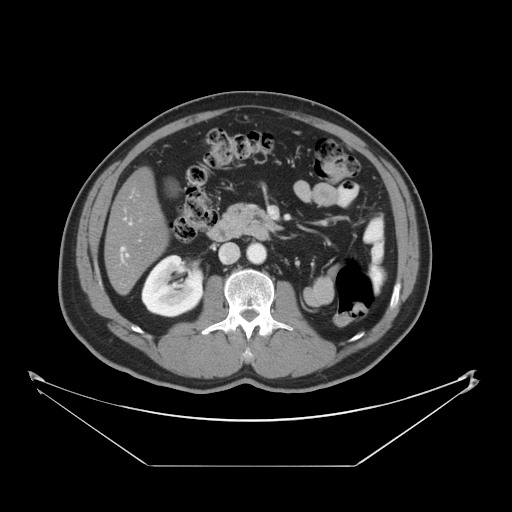
Contrast-enhanced abdominal CT, one axial slice; slice 16 of 46 in the series (ordered by position); reconstruction kernel STANDARD; 120 kVp; intravenous contrast given; soft-tissue window (W 400 / L 40 HU); 5 mm slice thickness; 512 × 512 image matrix, field of view 465 × 465 mm. Male patient, age 57 years. Case-level facts recorded for this patient, not image findings: diagnosis: colorectal cancer liver metastases, imaged before liver resection; multiple liver metastases: no; largest metastasis: 3.3 cm.
Annotated regions visible in this slice (manually delineated by an expert):
- hepatic veins: box from (x=121, y=247) to (x=124, y=250) px
- liver: (x=105, y=170)–(x=168, y=293)
- planned liver remnant (the part of the liver to remain after resection): (x=105, y=170)–(x=168, y=293)
- portal vein (with intrahepatic branches): (x=126, y=255)–(x=128, y=257)